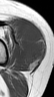
MRI of an extremity soft-tissue mass, one axial slice. Position 28 of 42 along the scan axis. MR volume resampled by the dataset authors to the PET/CT grid (not the native acquisition matrix). 3.27 mm slice thickness. 54 × 97 image matrix, field of view 53 × 95 mm. Female patient. From the clinical record (not read from this slice): histological type: spindle cell suggestive of biphasic synovial sarcoma; grade: intermediate; site of the primary tumour: left knee.
Outlined on this slice (expert contour drawn on MRI and transferred to this co-registered scan by the dataset authors):
- gross tumour volume including surrounding oedema: bounding box [x1, y1, x2, y2] px = [19, 19, 45, 65]
- gross tumour volume (mass): [19, 19, 45, 65]